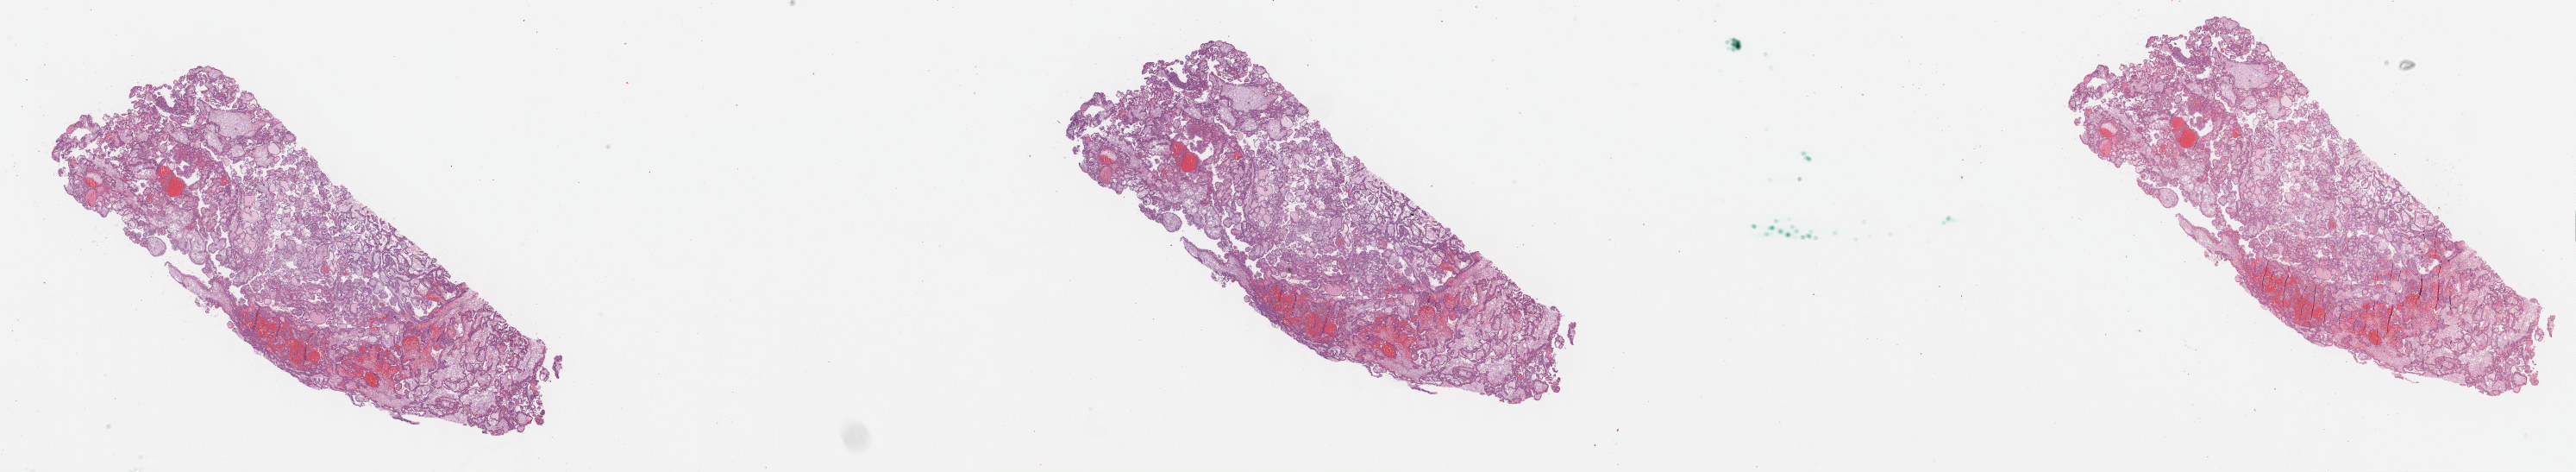
Hematoxylin and eosin (H&E) stained whole-slide image, whole scanned area (about 48.3 x 8.8 mm, from a 40x scan) shown as a low-resolution overview; FFPE section; primary tumour sample from the kidney. Patient: female, age at initial diagnosis 66 years.
Histologic diagnosis: Papillary adenocarcinoma, NOS.